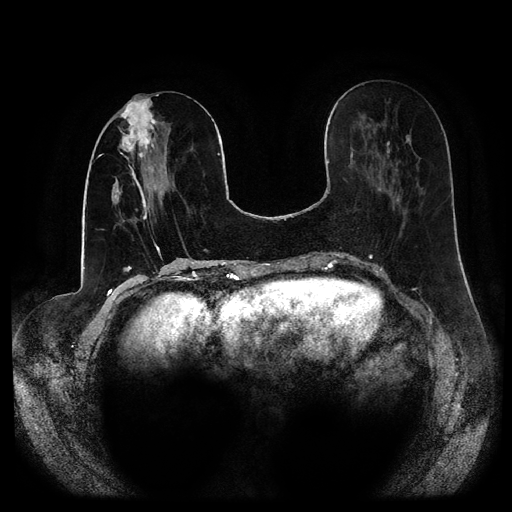
Breast MRI (dynamic contrast-enhanced, multi-phase), one axial slice; position 37 of 116 along the scan axis; dynamic contrast-enhanced series, time point 2 of 5 at this slice position (early post-contrast); 1.5 T; TE 2.6 ms, TR 5.2 ms; 2 mm slice thickness; 512 × 512 image matrix, field of view 380 × 380 mm. Patient: female, 53 years.
Outlined on this slice (semi-automatically segmented with operator editing):
- breast lesion (labelled 'tumour' in the annotation; benign lesions carry a separate 'benign' label): bounding box [x1, y1, x2, y2] px = [118, 96, 160, 159]